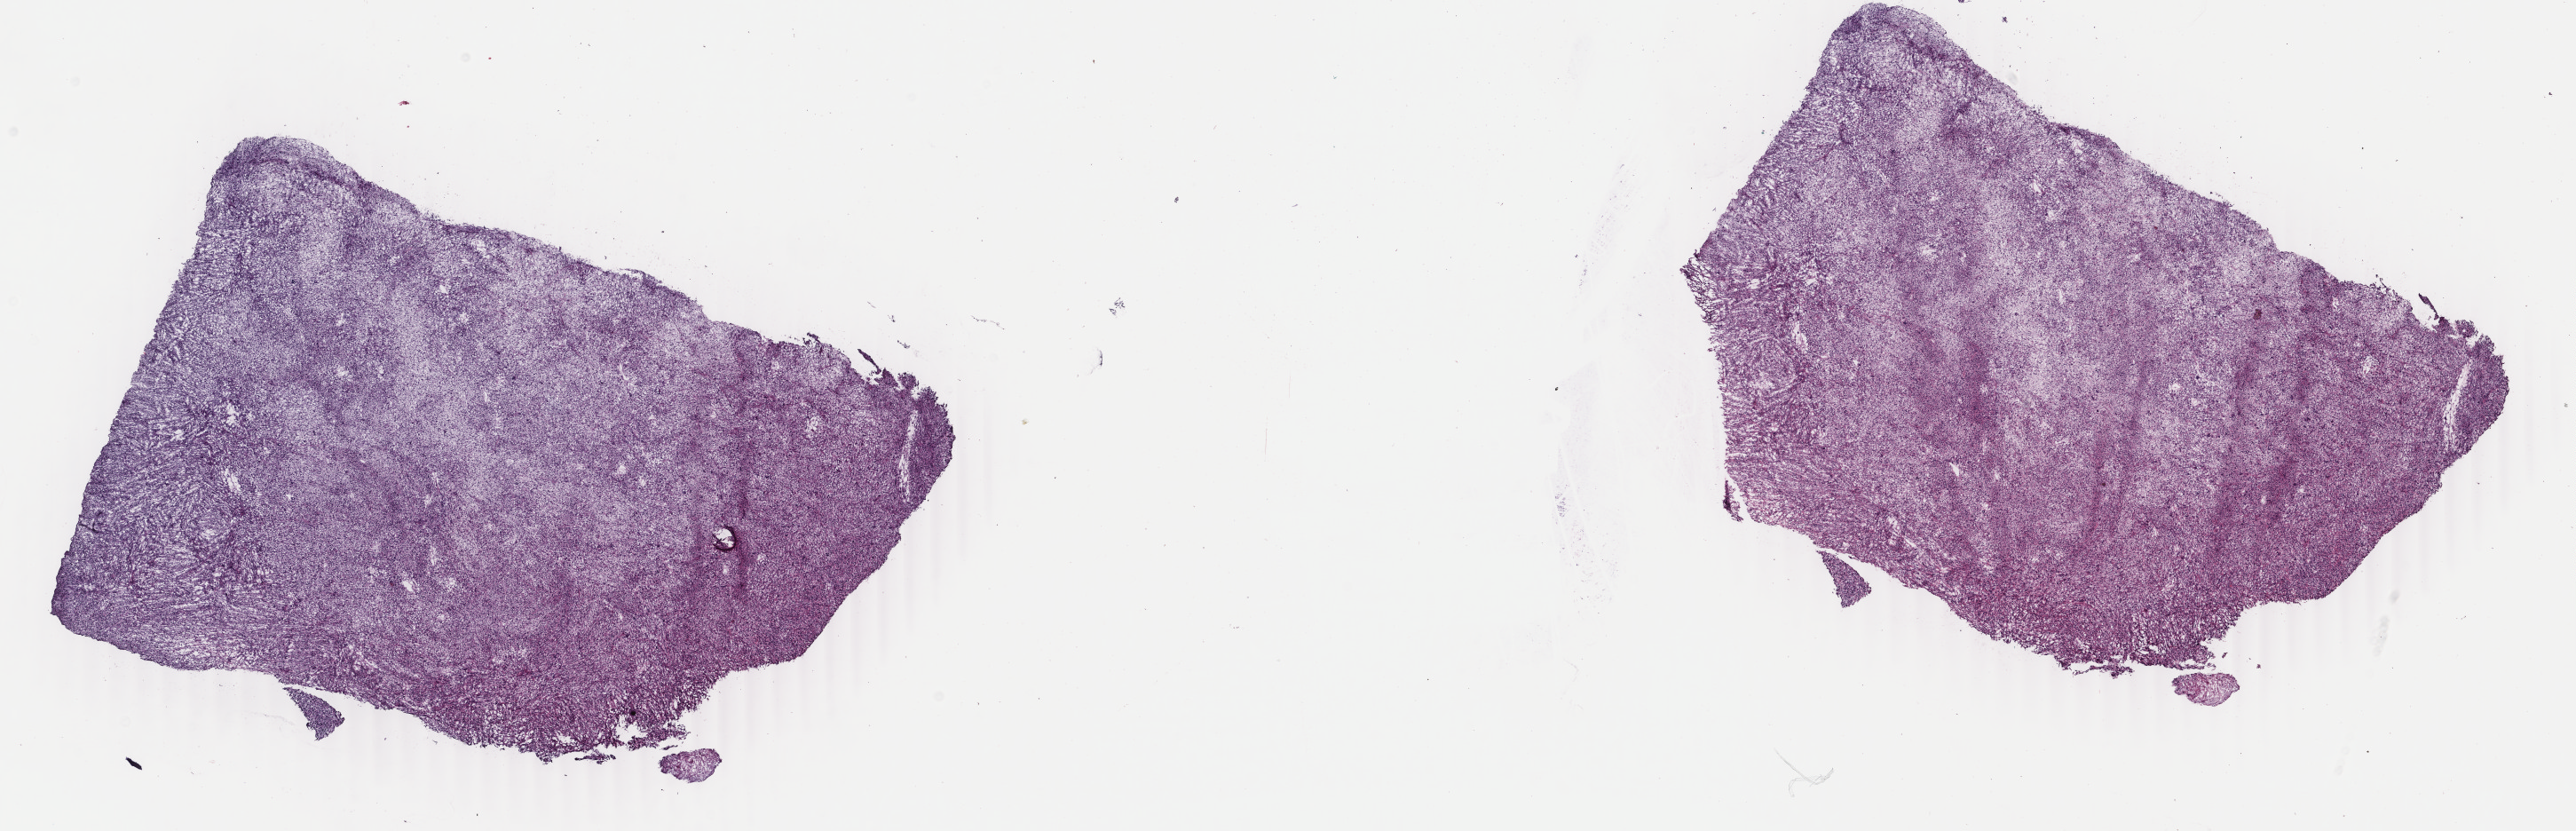
Digitized Hematoxylin and eosin (H&E) stained tissue section (whole slide), a low-resolution overview of the entire scanned area, about 23.1 x 7.4 mm (slide scanned at 40x). Frozen section from the top of the tissue portion. Retroperitoneum and peritoneum, primary tumour sample. Male patient; age at initial diagnosis 80 years. Slide review estimates, as recorded: tumour cells 90%, tumour nuclei 90%, normal cells 0%, stromal cells 10%, necrosis 0%. Inflammatory infiltration, as recorded: lymphocyte infiltration 0%, monocyte infiltration 0%, neutrophil infiltration 0%.
- pathologic diagnosis: Dedifferentiated liposarcoma (retroperitoneum)